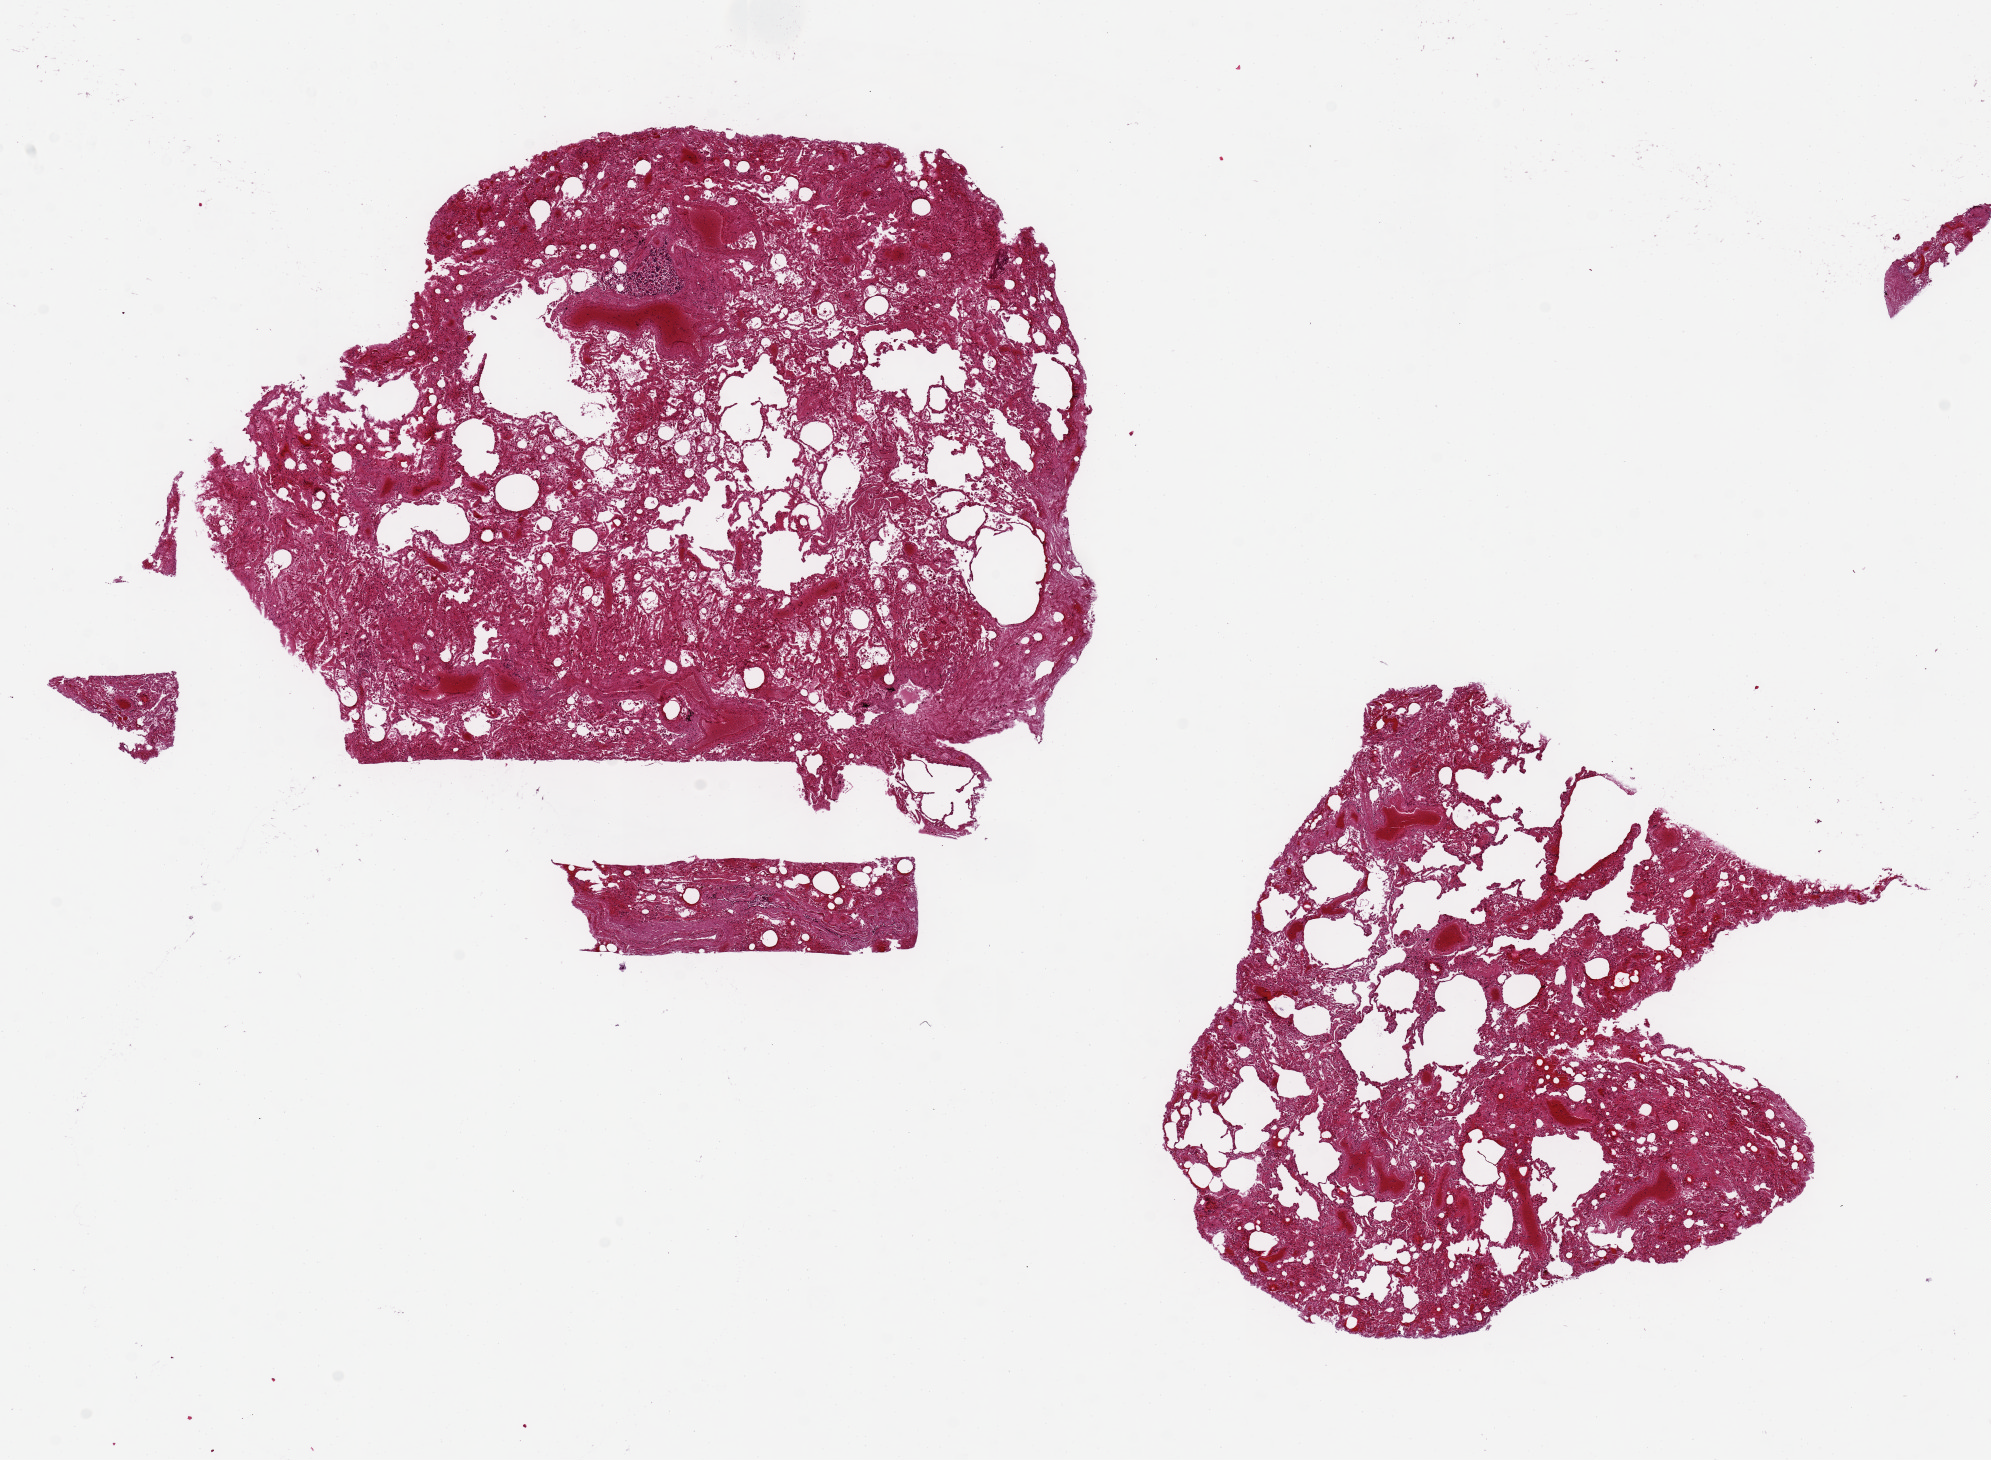
Haematoxylin and eosin whole-slide image — shown as a low-resolution overview of the whole scanned area (about 15.8 x 11.5 mm), PAXgene-fixed, paraffin-embedded tissue, sampled site (target tissue): lung, donor tissue sample. Donor sex: male.
Pathologist's review note for this sample: 2 pieces severe probable congestion but severly autolyzed tissue hampers interpretation, ~7x5mm.